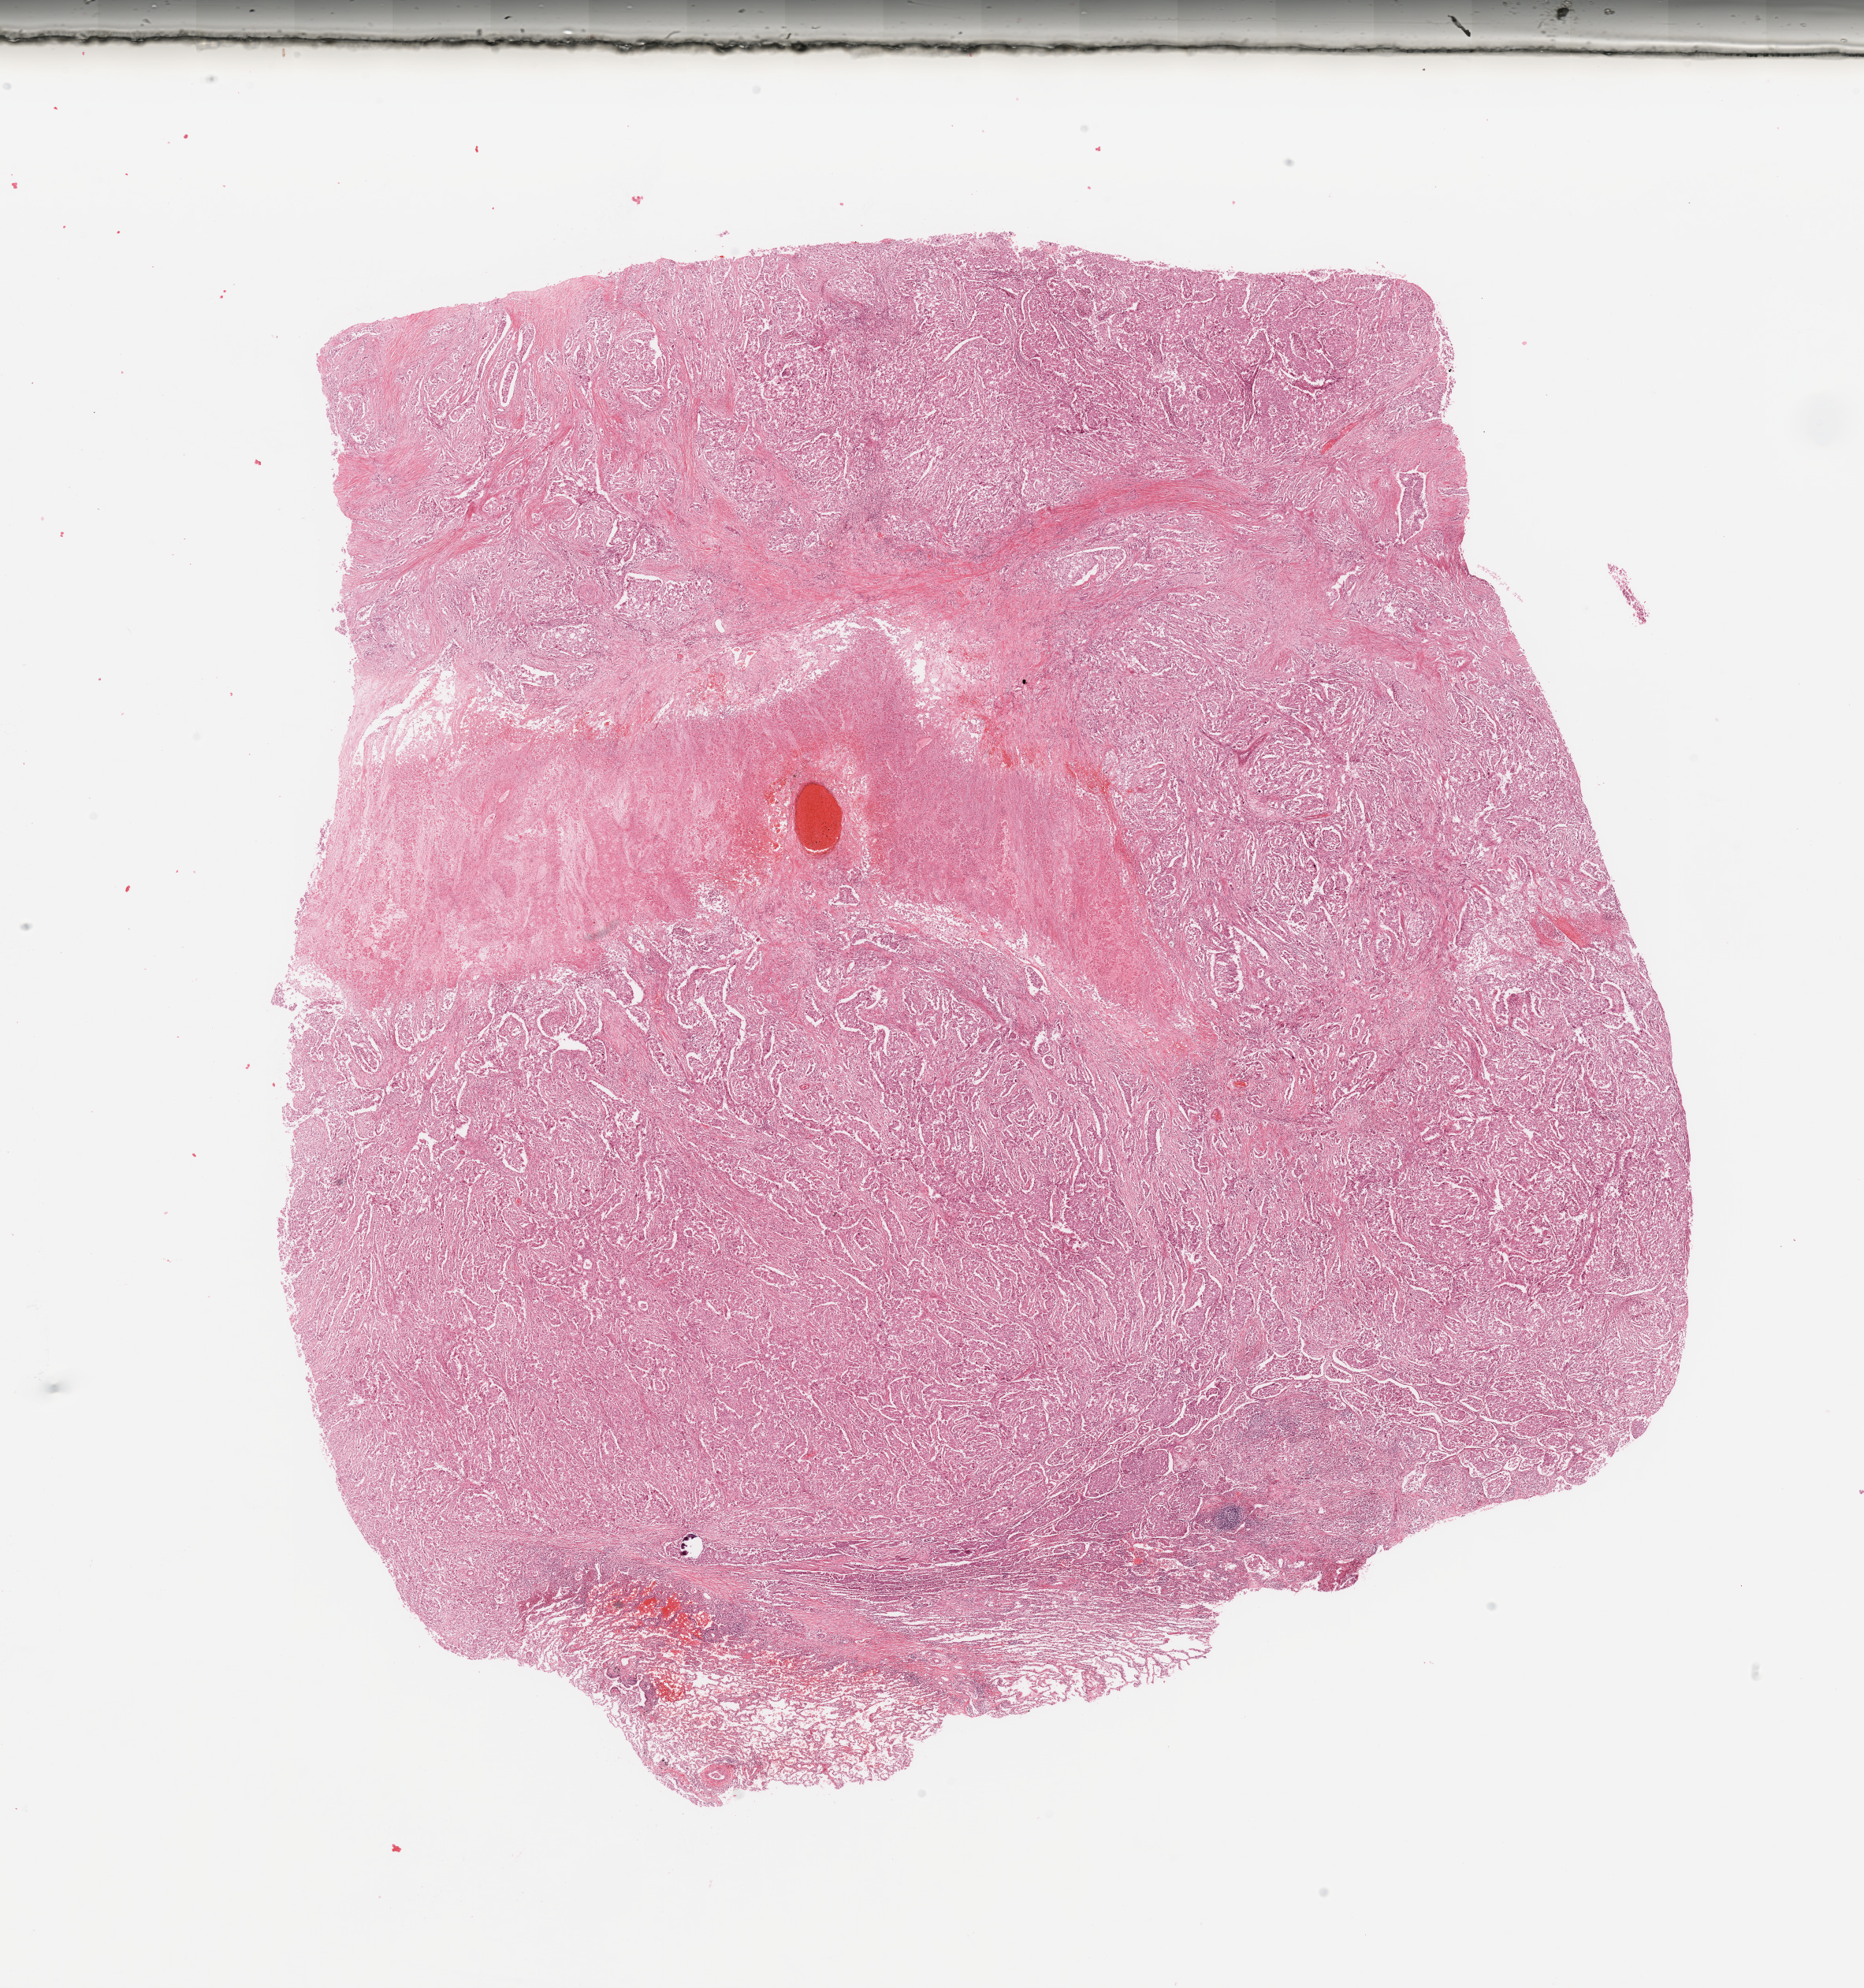
H&E whole-slide image, whole scanned area (about 18.7 x 19.9 mm) shown as a low-resolution overview, lung, tumour tissue. 49-year-old female patient.
Histologic diagnosis: Adenocarcinoma, NOS.